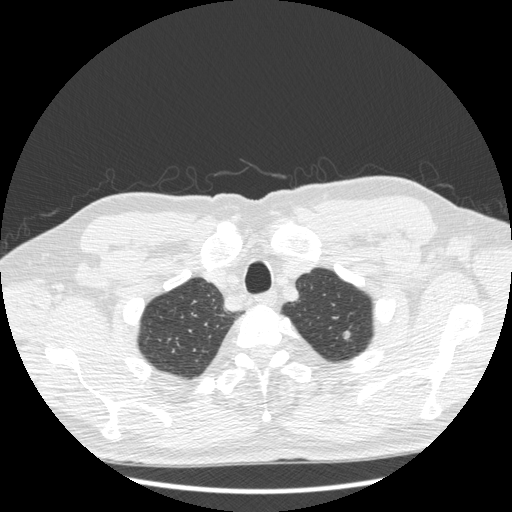
Axial slice from a low-dose chest CT screening exam, third screening round (two years after baseline), lung window (W 1500 / L -600 HU), 1.25 mm slice thickness, standard (soft-tissue) reconstruction kernel (STANDARD), slice 30 of 223 in the series, 512 × 512 image matrix, field of view 380 × 380 mm. Male participant, aged 69 years at enrolment. Former smoker at enrolment.
- Lesion marked by an expert reader, bounding box [x1, y1, x2, y2] px = [330, 321, 361, 346].
- Reader record for this screening exam (exam-level; its link to the box is not recorded): non-calcified nodule or mass ≥4 mm, left upper lobe, 7 × 6 mm, smooth margins, soft tissue attenuation, pre-existing on the prior screen: yes; interval growth: yes.
- Official screen result: positive, other.
- Participant outcome: lung cancer diagnosed 112 days after this screen — adenocarcinoma, NOS, left upper lobe, moderately differentiated (G2), stage IA (AJCC 6th edition), 10 mm at pathology.